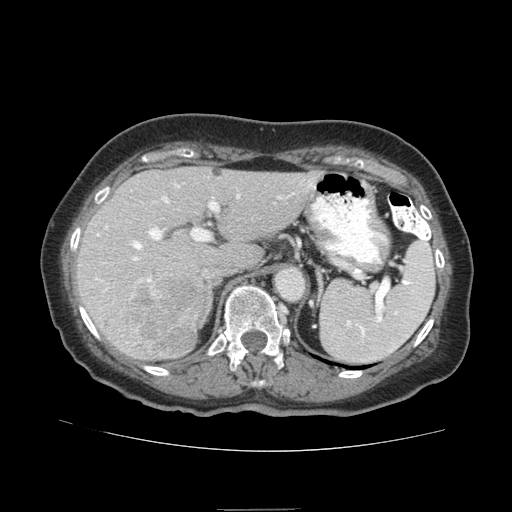
Contrast-enhanced abdominal CT (liver protocol), one axial slice; slice 51 of 95 in the series (ordered by position); 140 kVp; soft-tissue window (W 400 / L 40 HU); 2.5 mm slice thickness; 512 × 512 image matrix, field of view 360 × 360 mm. From the clinical record (not read from this slice): diagnosis: hepatocellular carcinoma (patient treated with transarterial chemoembolisation; whether this scan precedes or follows treatment is not stated here); TNM stage (as recorded): Stage-IVA; Child-Pugh class: B.
Structures marked on this image (semi-automatic segmentation, software-assisted and operator-edited):
- liver parenchyma outside the tumour (the mass and vessels are separate outlines, so this box may not span the whole liver): box from (x=76, y=166) to (x=322, y=360) px
- mass: (x=131, y=275)–(x=205, y=355)
- liver vessels: (x=96, y=183)–(x=313, y=282)